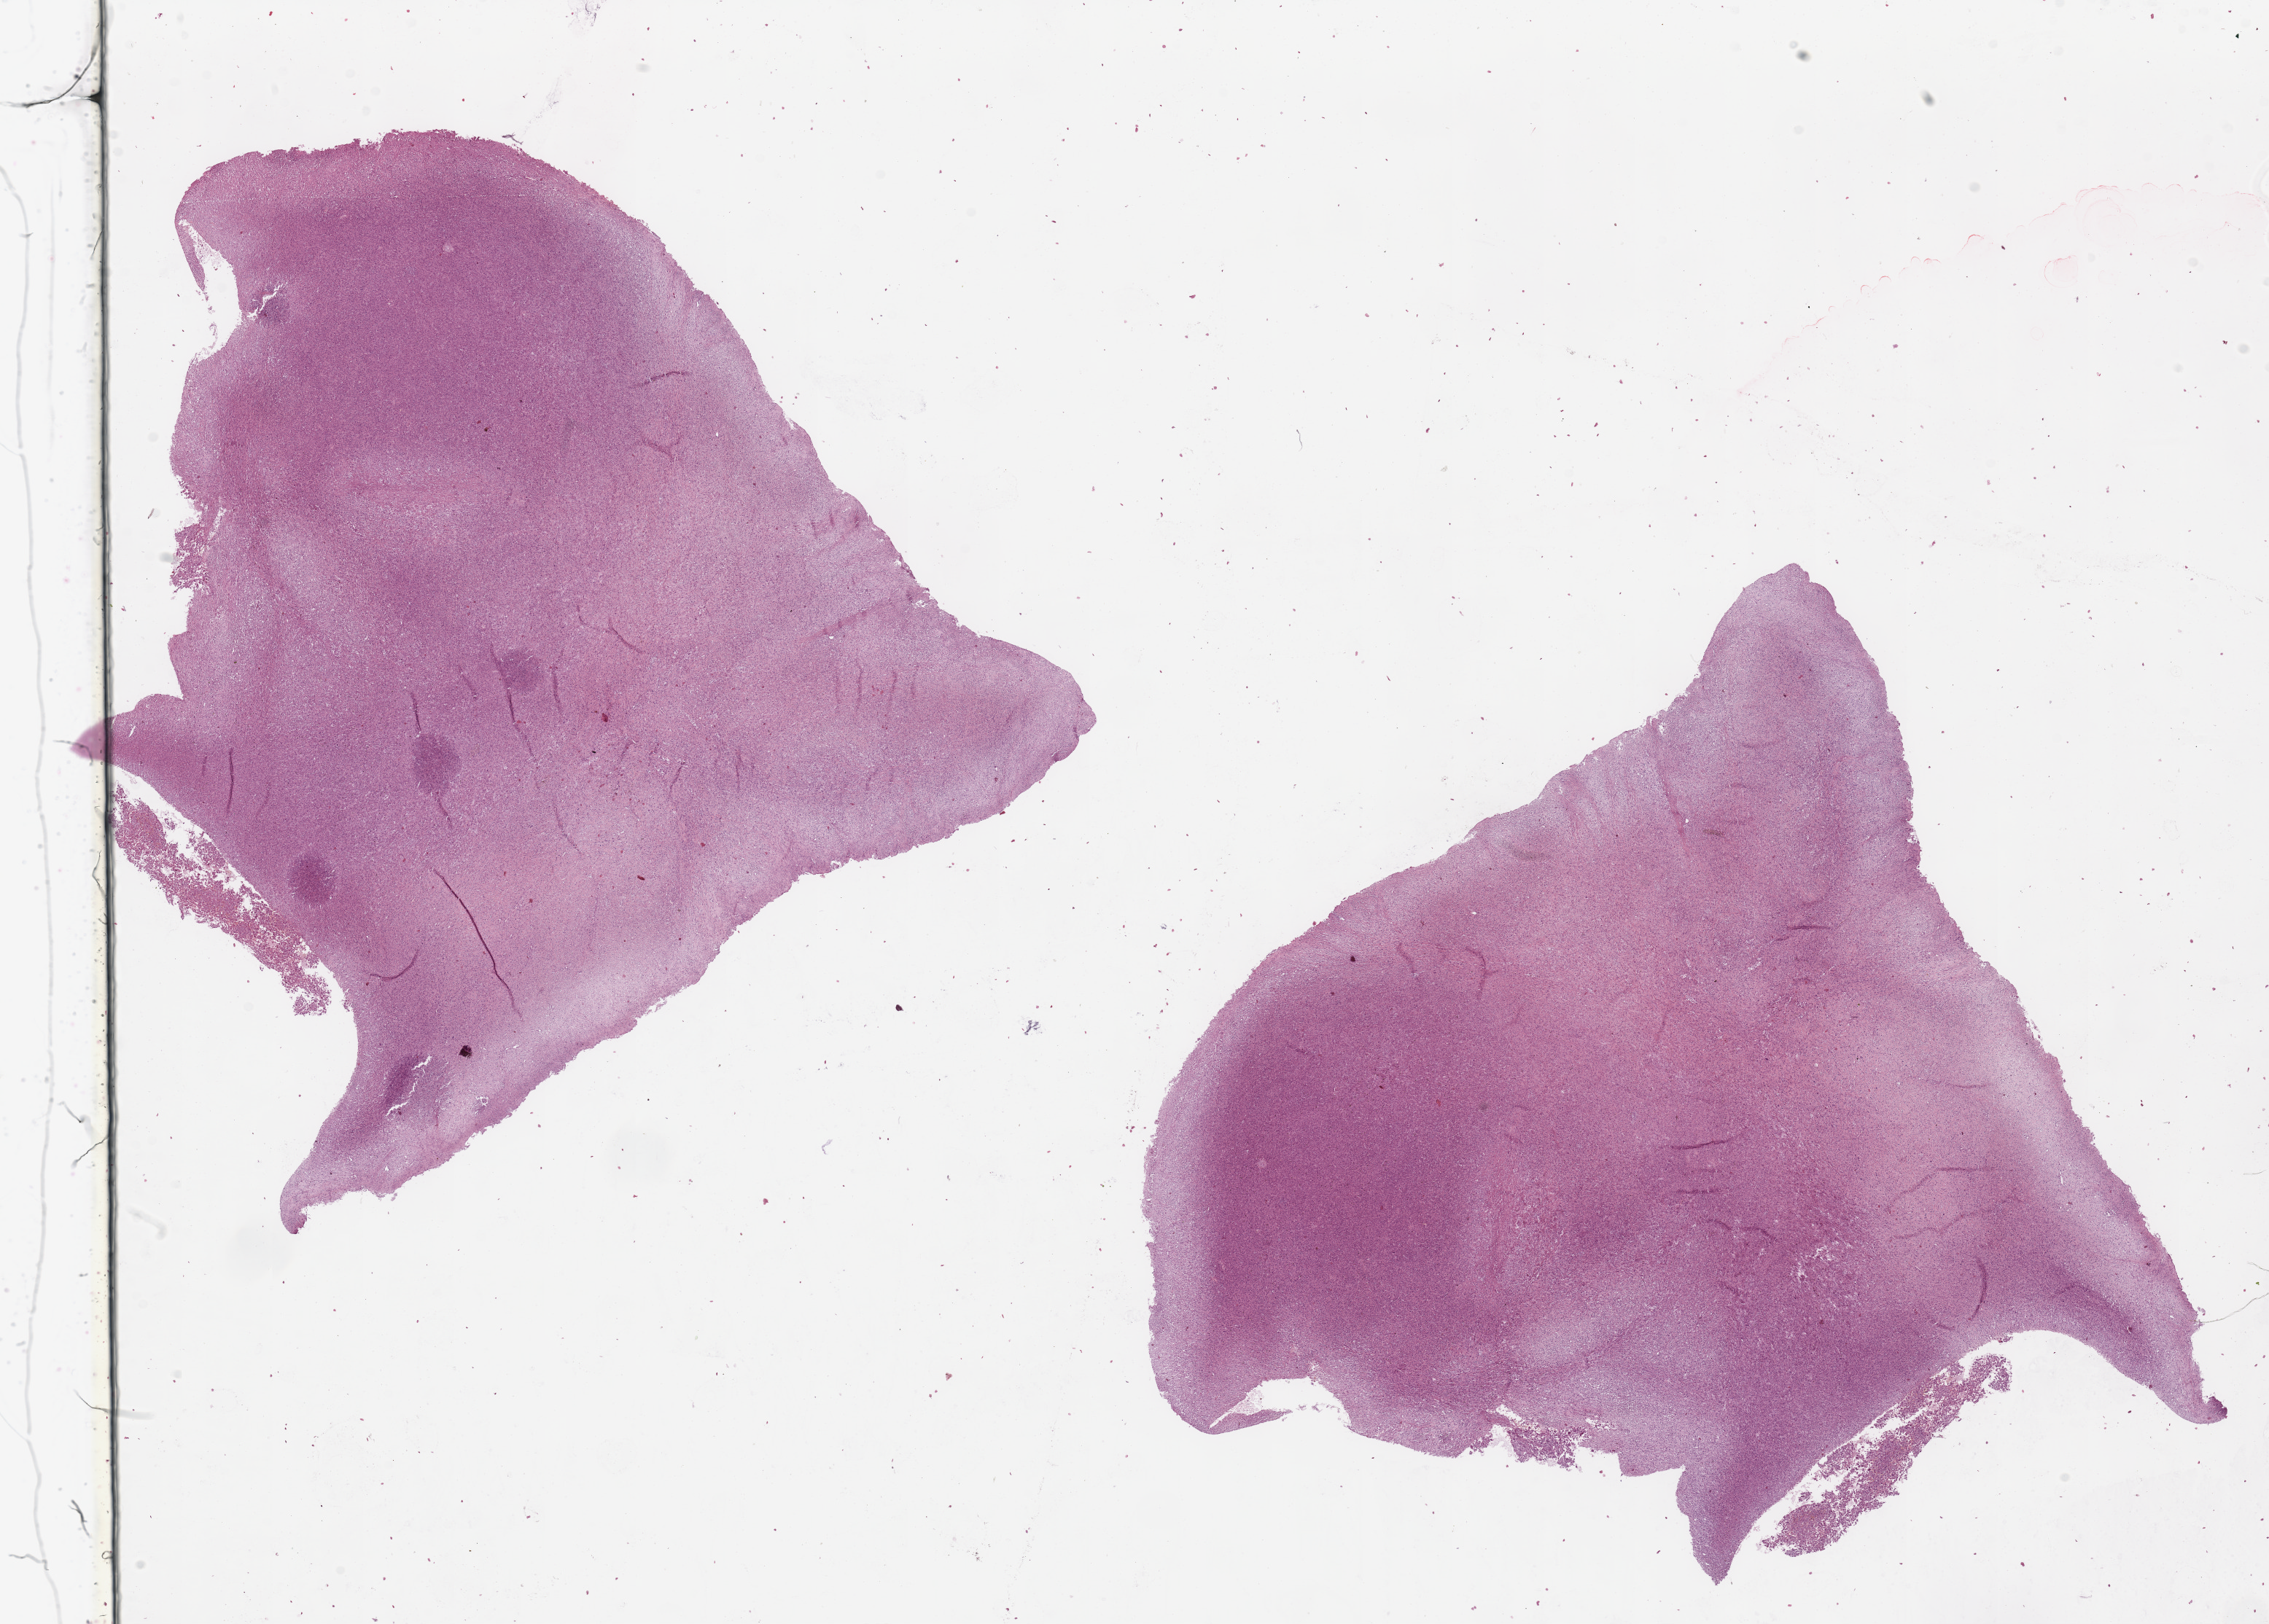
H&E whole-slide image, a low-resolution overview of the entire scanned area, about 24.6 x 17.6 mm (from a 20x scan); tumour tissue sample. Female, 50 y/o.
Patient diagnosis (cohort enrolment): sarcoma (site not recorded at cohort level). Primary tumour site (as recorded): lower extremity.